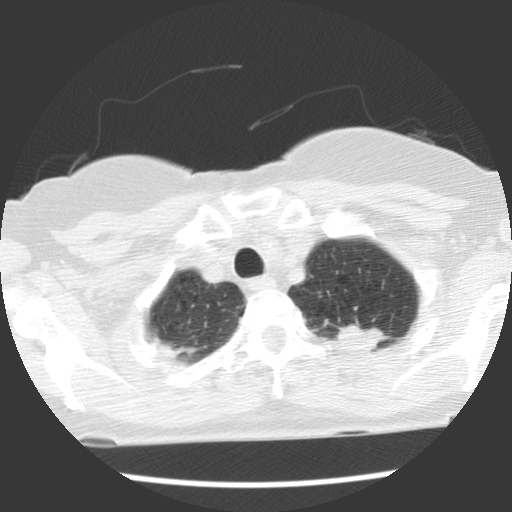
Low-dose screening chest CT, one axial slice; lung window (W 1500 / L -600 HU); 2.5 mm slice thickness; 512 × 512 image matrix, field of view 300 × 300 mm.
Outlined on this slice (expert manual segmentation):
- lesion 1 (tumor, upper lobe of left lung): box from (x=337, y=322) to (x=388, y=350) px